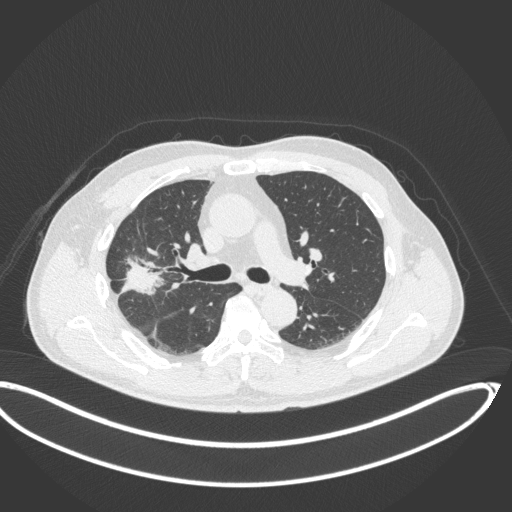
Chest CT, one axial slice. Position 213 of 341 along the scan axis. Reconstruction kernel B31f. Lung window (W 1500 / L -600 HU). 1 mm slice thickness. 512 × 512 image matrix, field of view 439 × 439 mm. Male patient, age 63 years. From the clinical record (not read from this slice): clinical TNM (as recorded): T1c N0 M0; histopathological grade: G2-3.
Structures marked on this image (bounding box drawn by a radiologist):
- lung tumour (recorded histology: adenocarcinoma): bounding box (x1, y1, x2, y2) in pixels: (119, 253, 162, 303)